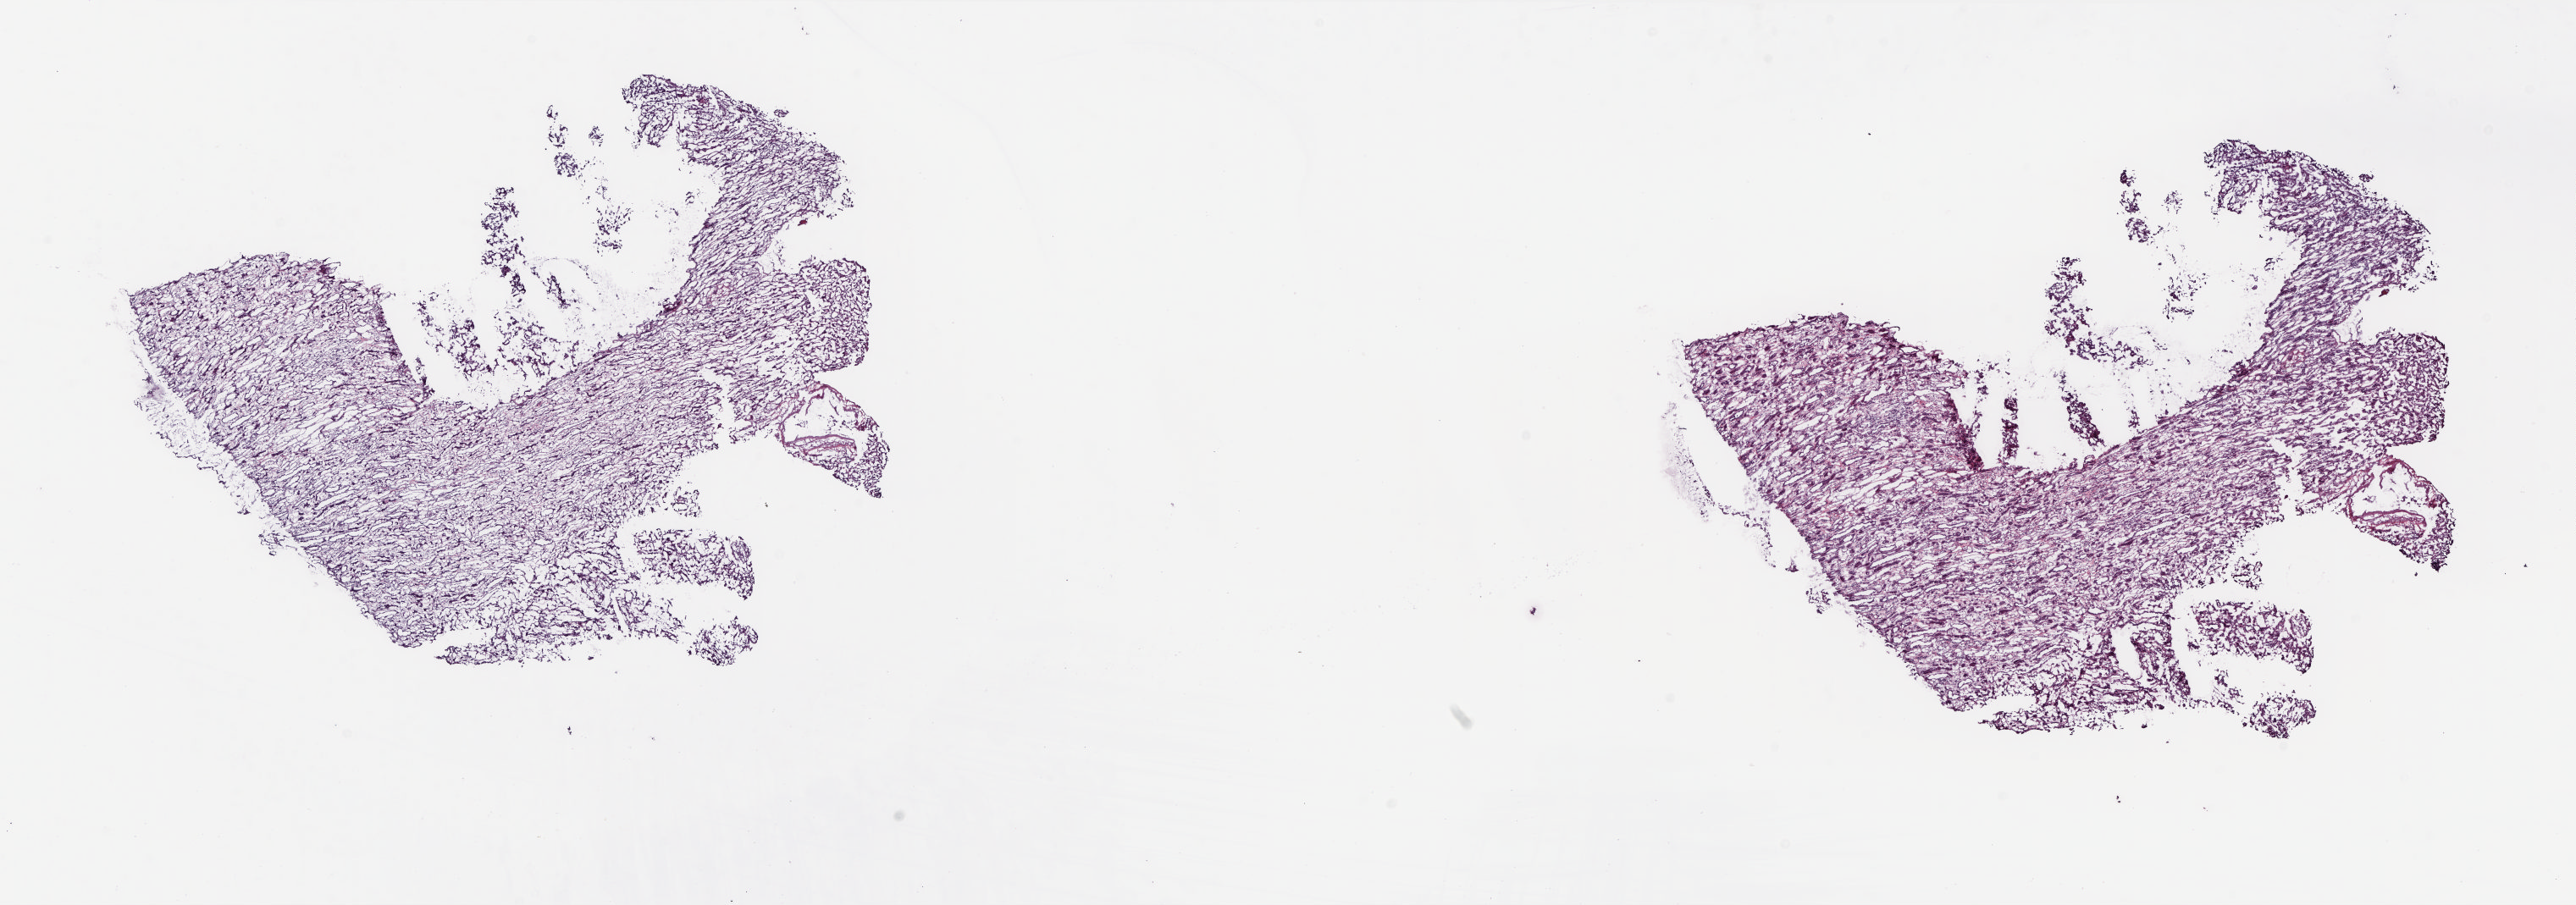
Whole-slide histology image, Hematoxylin and eosin (H&E) stained, whole scanned area (about 24.5 x 8.6 mm, slide scanned at 20x) shown as a low-resolution overview; frozen section from the top of the tissue portion; sample: solid tissue normal (non-tumour tissue), adrenal cortex. Female, age 44 years at initial diagnosis. Slide review estimates, as recorded: tumour cells 0%, tumour nuclei 0%, normal cells 100%, stromal cells 0%, necrosis 0%. Infiltration values recorded for this section: lymphocyte infiltration 1%, monocyte infiltration 0%, neutrophil infiltration 0%.
- this section: solid tissue normal sample (biorepository sample class)
- patient diagnosis: Adrenal cortical carcinoma (cortex of adrenal gland)